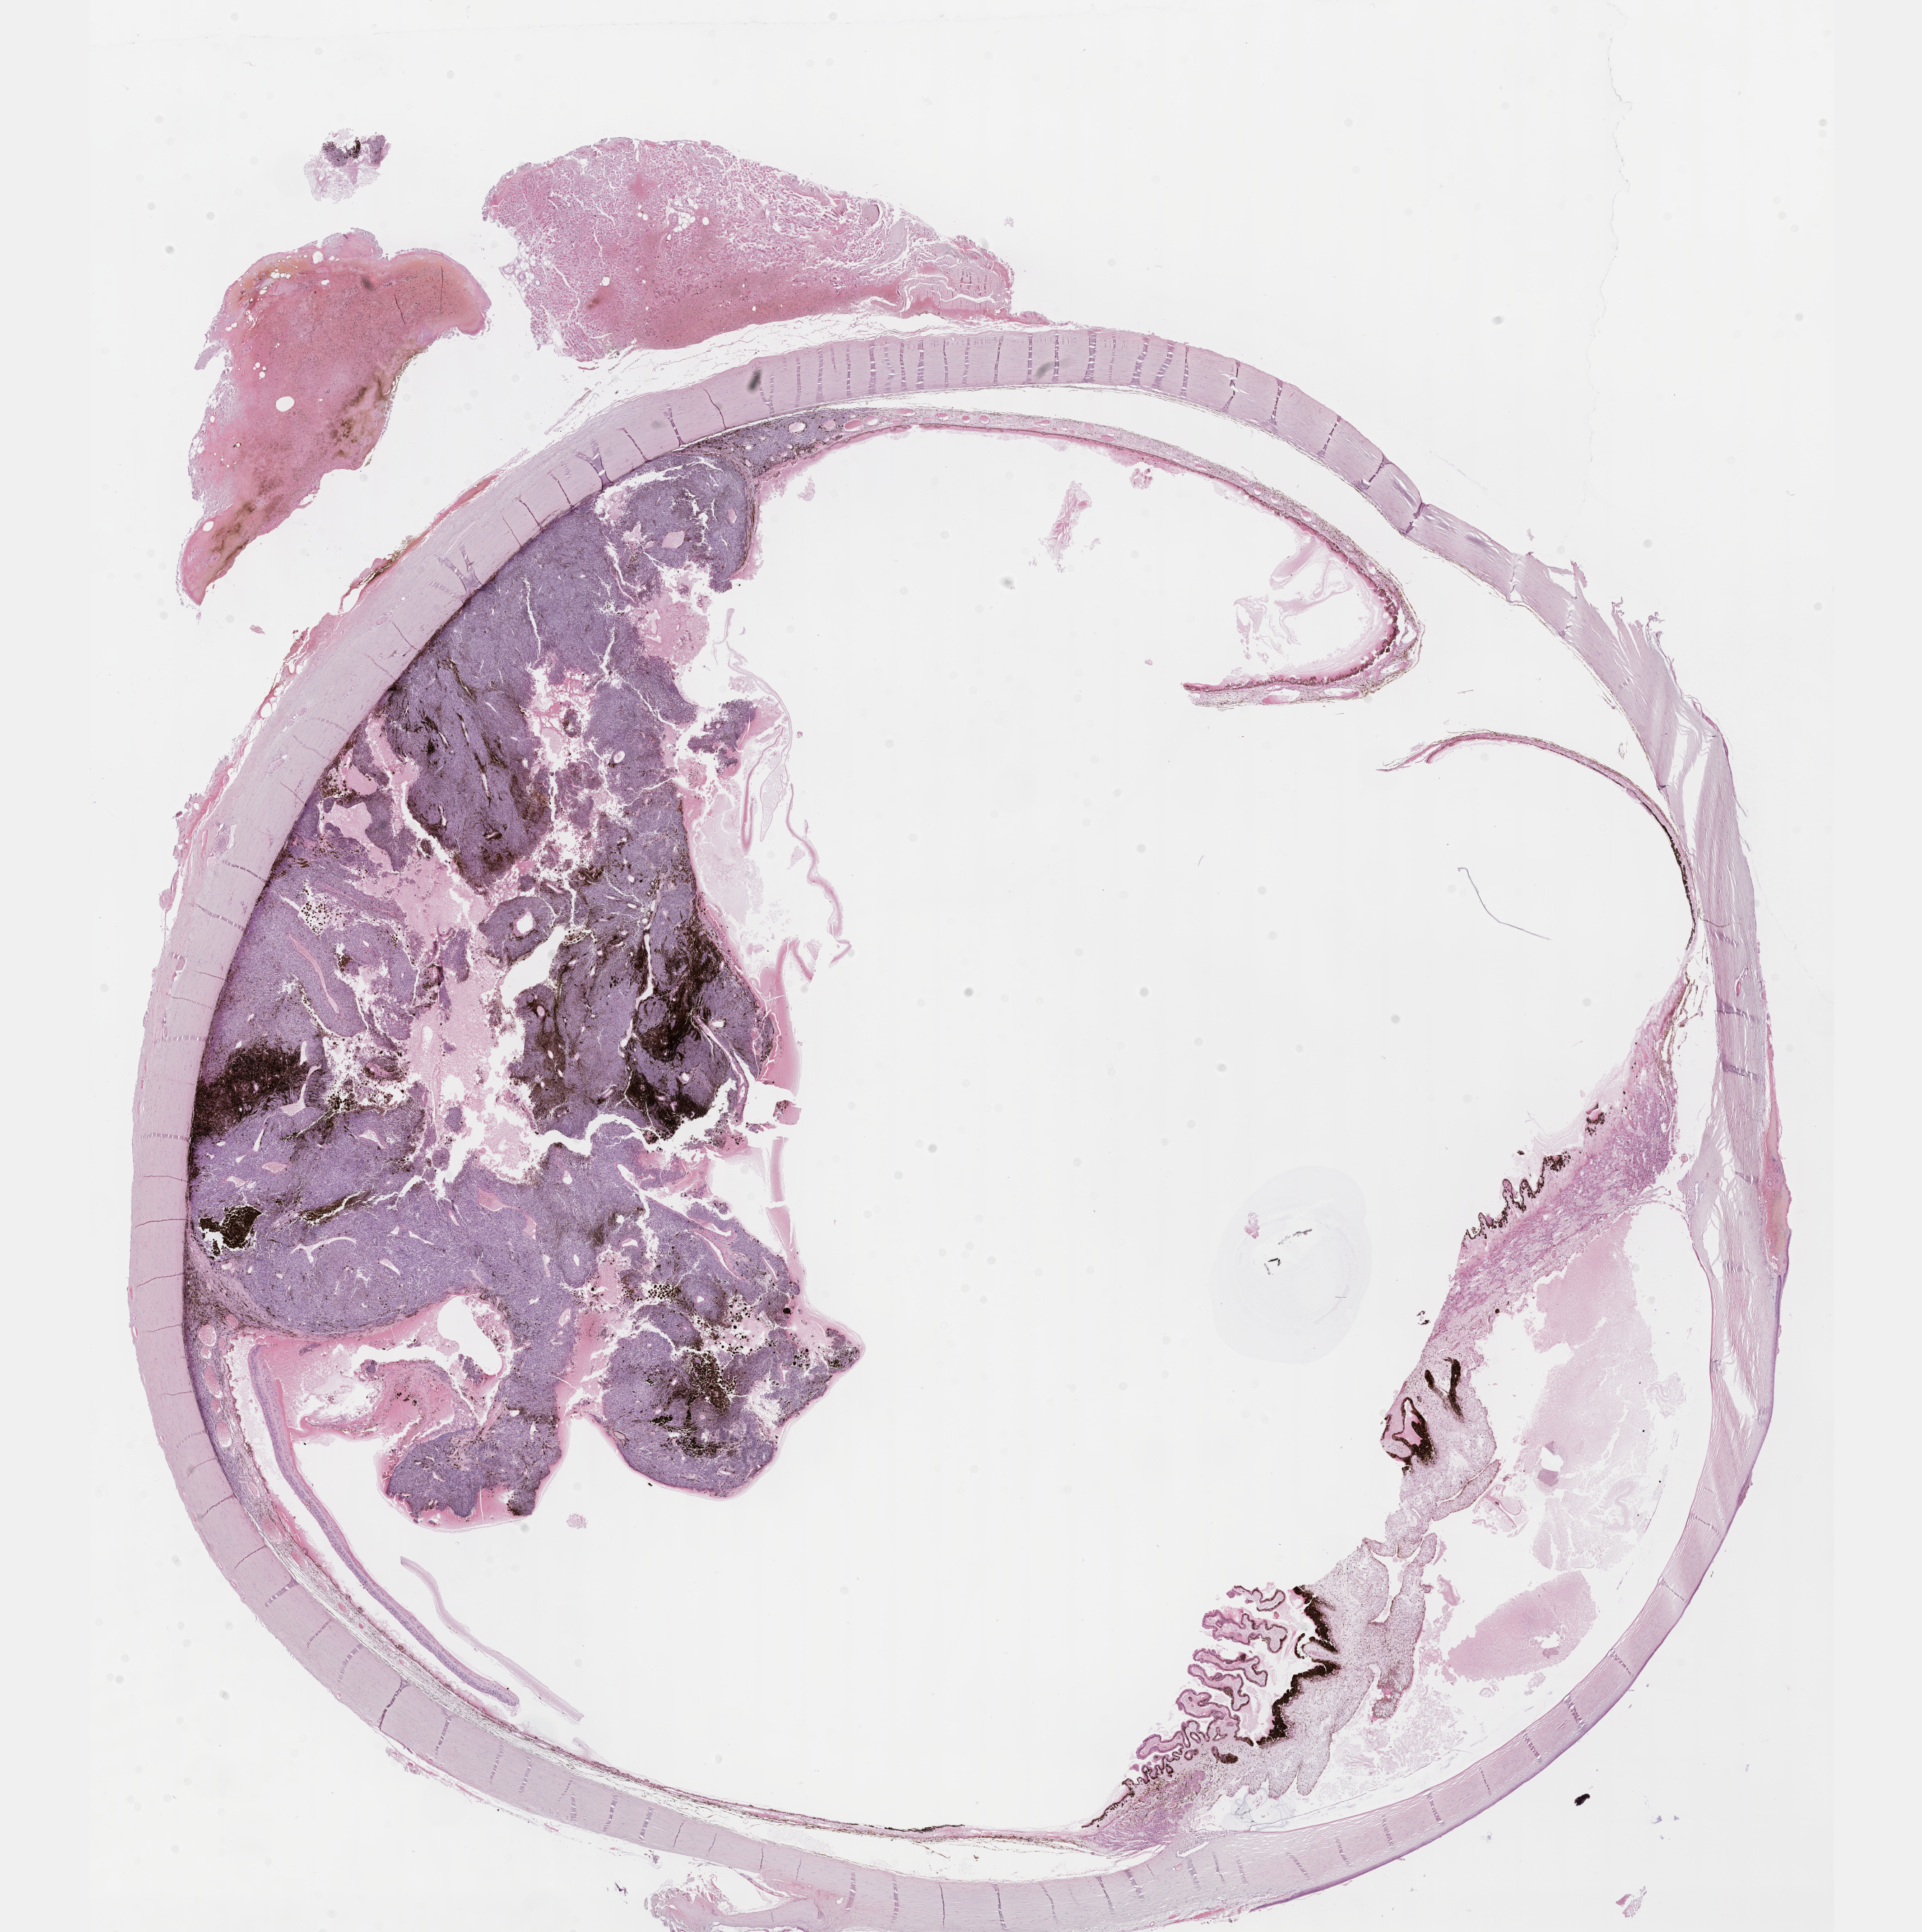
Digitized H&E tissue section (whole slide), low-resolution overview of the scanned area, about 21.6 x 21.7 mm (acquisition: 40x scan), formalin-fixed paraffin-embedded (FFPE) diagnostic section, primary tumour sample from the uvea. Patient: male, age at initial diagnosis 66 years.
- AJCC pathologic stage: IIIA
- TNM: T4a N0 M0
- histologic diagnosis: Spindle cell melanoma, NOS (choroid)